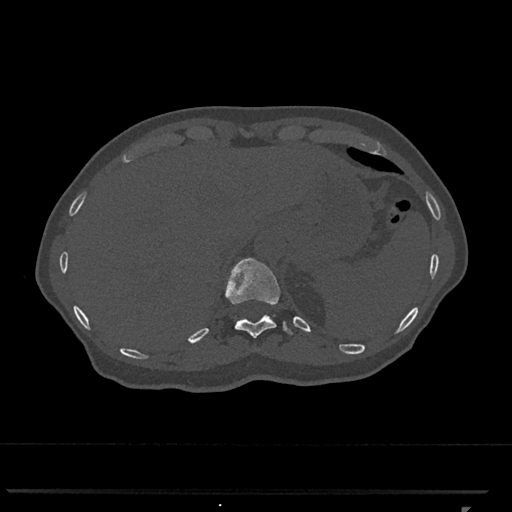
CT including the spine, one axial slice. Slice 512 of 793 in the series (ordered by position). Reconstruction kernel Br40s/3. Bone window (W 1800 / L 400 HU). 0.5 mm slice thickness. 512 × 512 image matrix, field of view 380 × 380 mm. Patient: female, 62 years. Case-level facts recorded for this patient, not image findings: primary cancer: renal.
Structures marked on this image (semi-automatic segmentation, software-assisted and operator-edited):
- T11 vertebra: box from (x=225, y=258) to (x=293, y=338) px